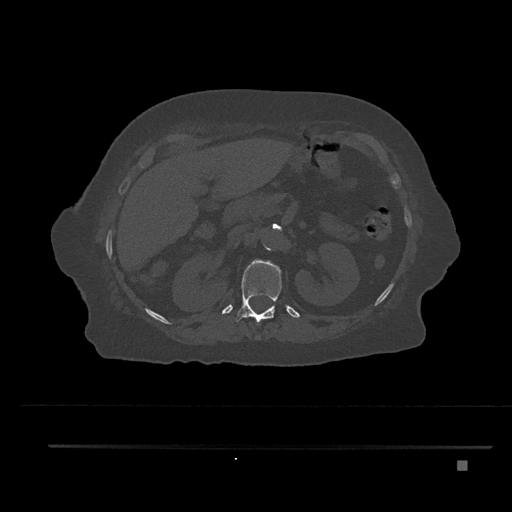
CT including the spine, one axial slice. Position 261 of 797 along the scan axis. Reconstruction kernel Br40s/3. 120 kVp. Bone window (W 1800 / L 400 HU). 0.5 mm slice thickness. 512 × 512 image matrix, field of view 437 × 437 mm. Patient: female, 76 years. From the clinical record (not read from this slice): primary cancer: lung.
Annotated regions visible in this slice (semi-automatically segmented with operator editing):
- T12 vertebra: bounding box [x1, y1, x2, y2] px = [235, 259, 282, 338]